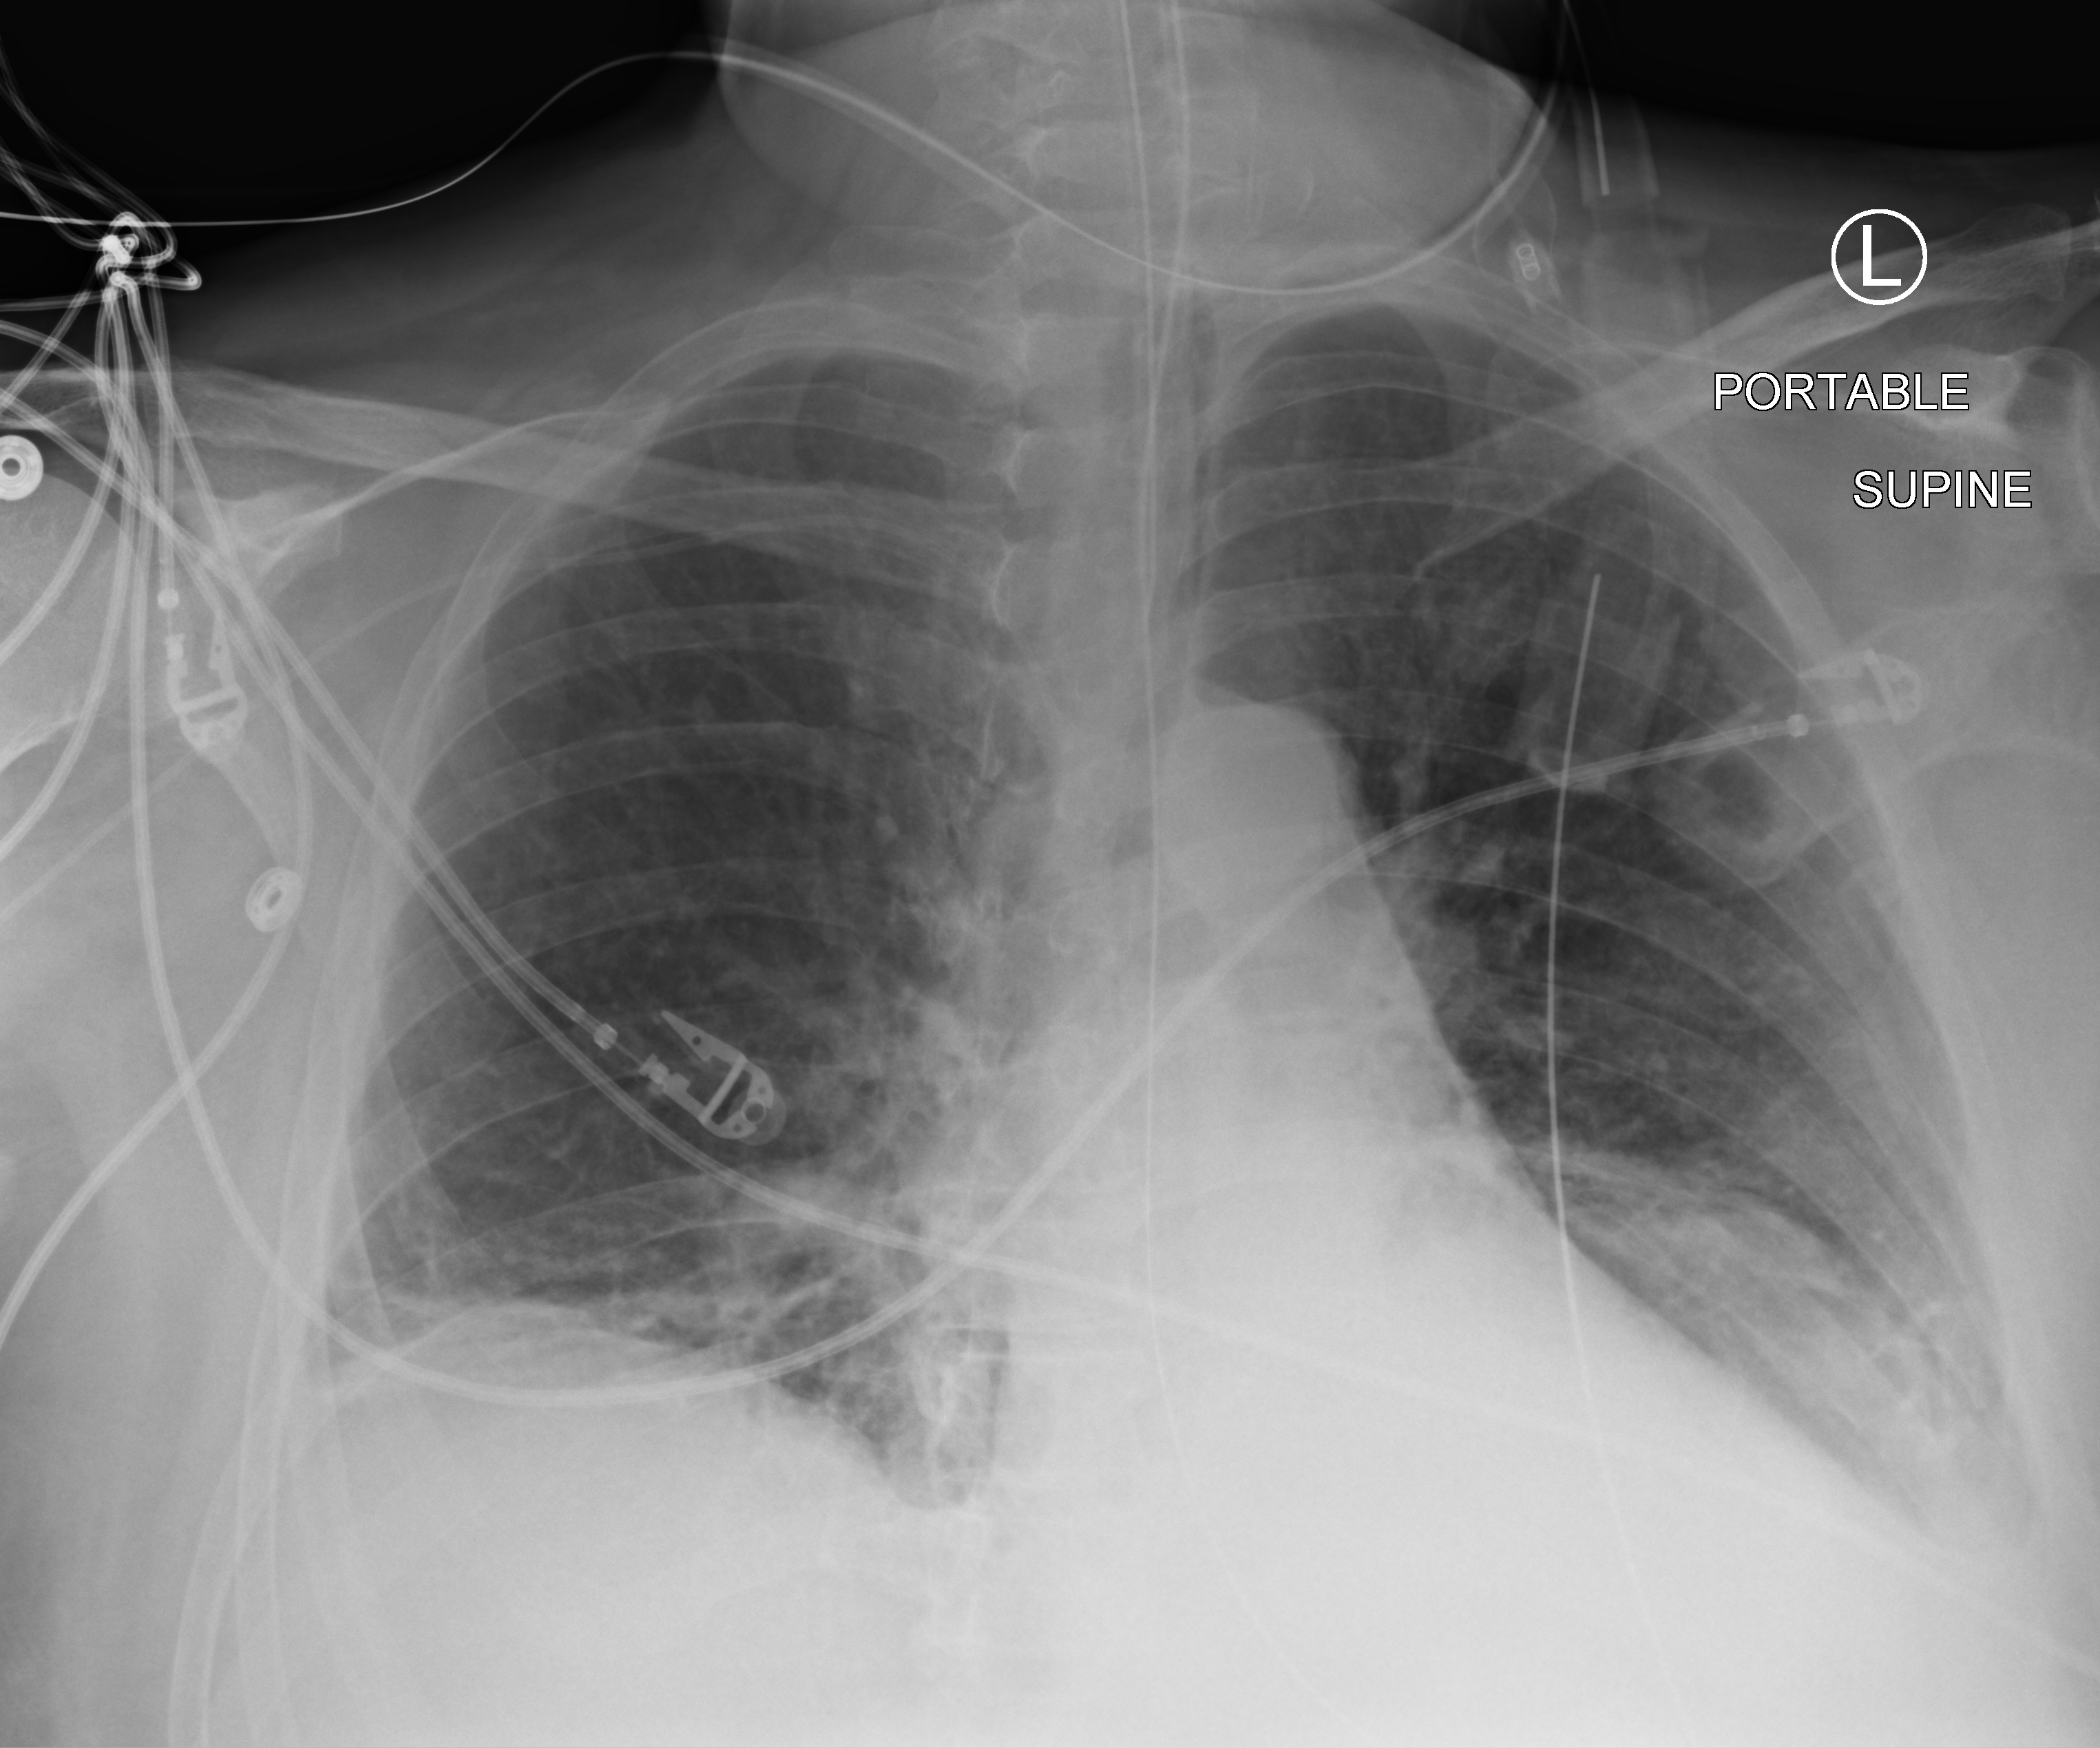
Chest X-ray (portable), anteroposterior (AP) projection. Patient hospitalised with COVID-19; male, aged 60–74 years.
Hospital-stay facts (about this admission, not read from this image; timing relative to this image not recorded): admitted to intensive care during this hospital stay: yes; other chronic lung disease (admission record): no.